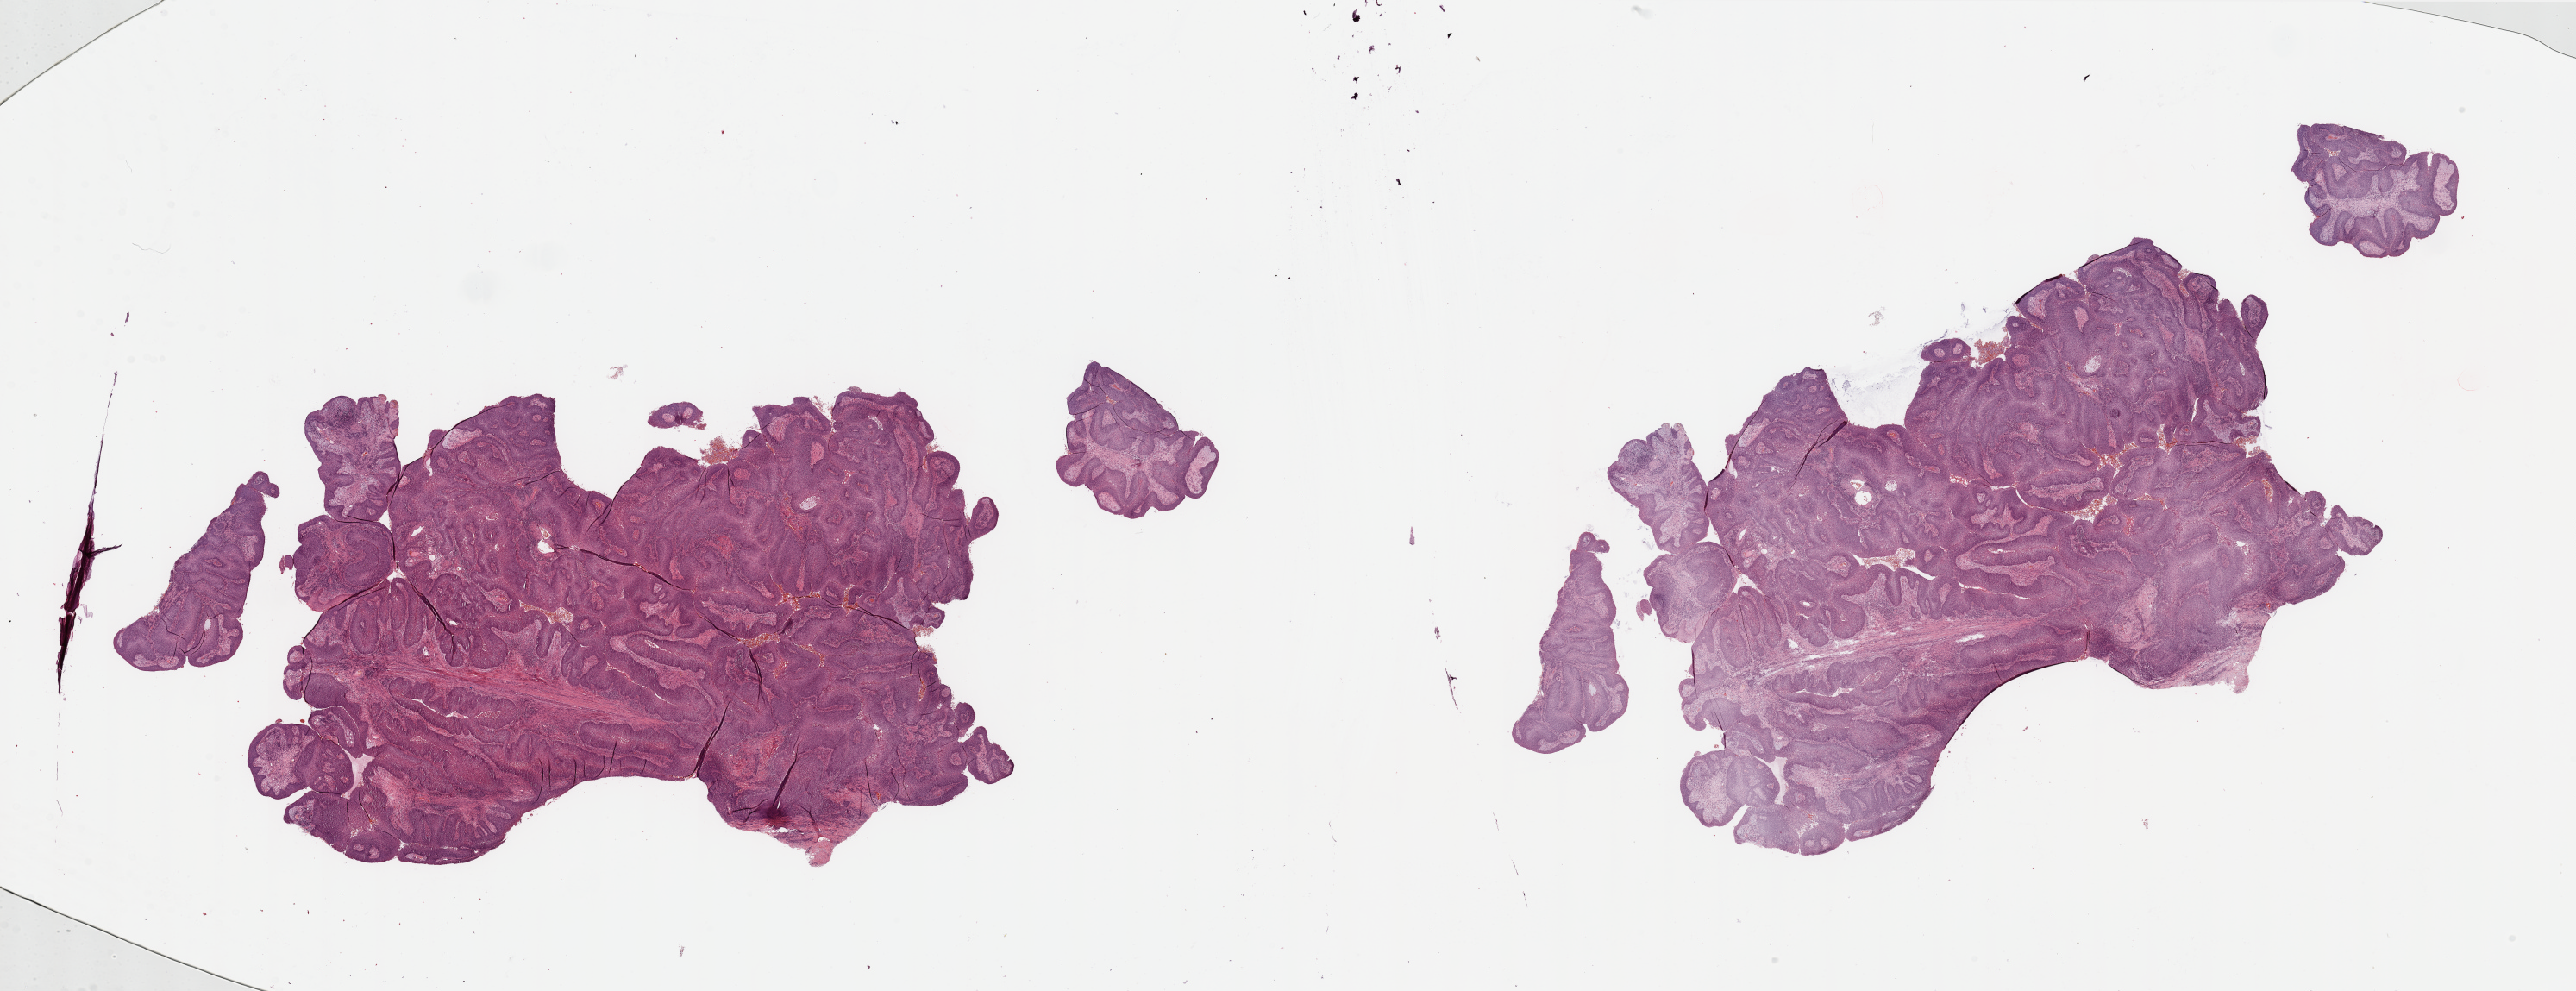
Digitized H&E tissue section (whole slide) — shown as a low-resolution overview of the whole scanned area (about 47.3 x 18.2 mm, slide scanned at 20x), tumour tissue sample, lung. 68-year-old male patient.
• patient diagnosis (cohort enrolment): squamous cell carcinoma (lung)